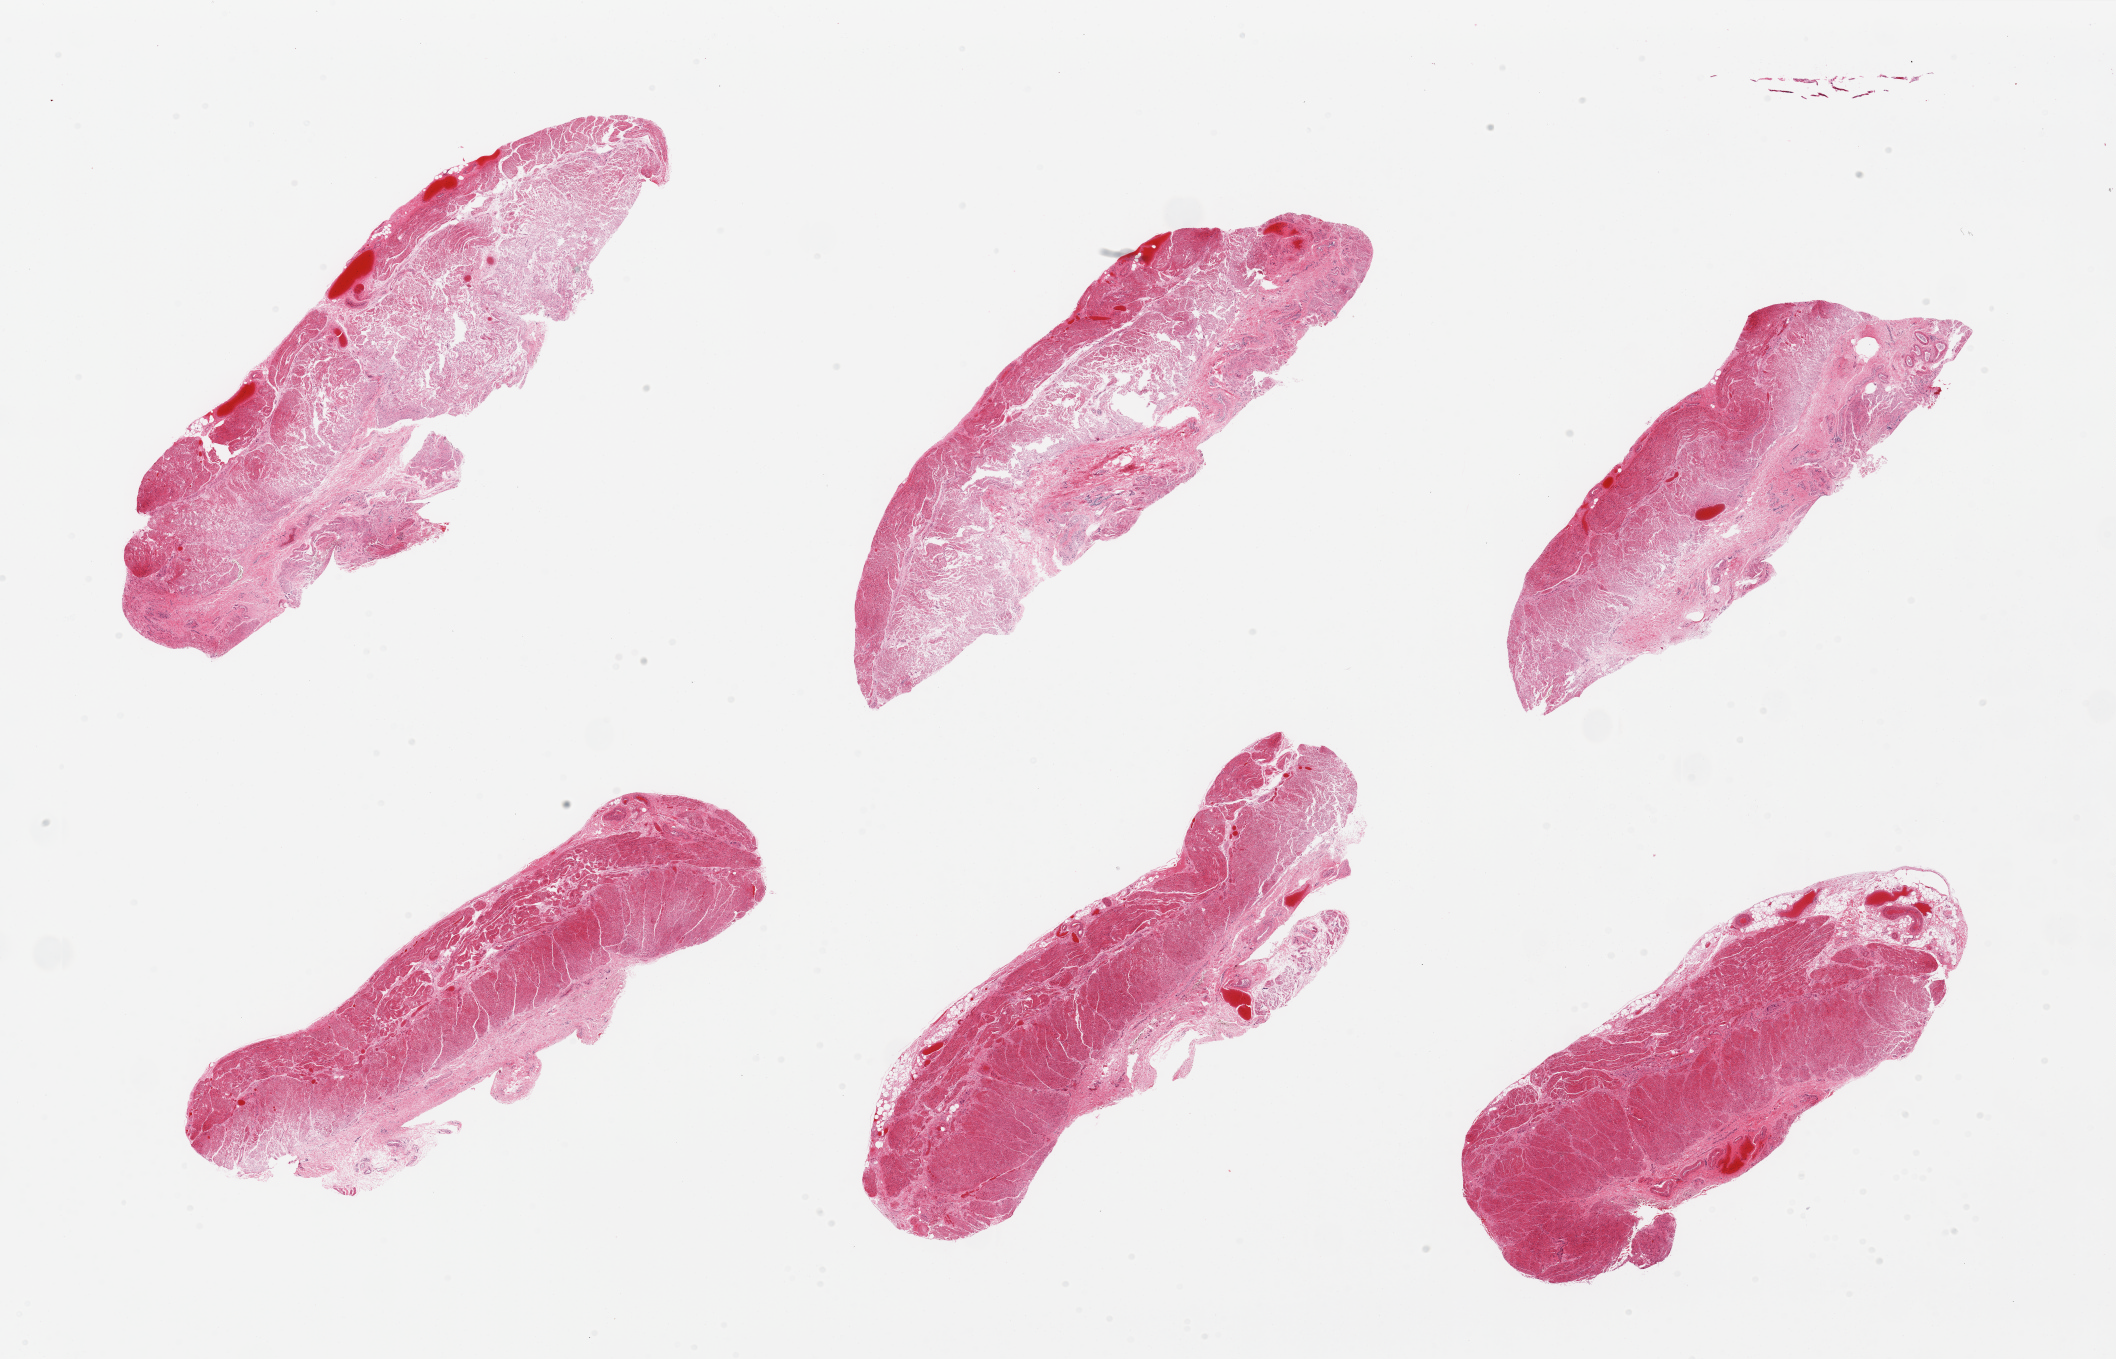
Digitized hematoxylin and eosin (H&E)-stained section, brightfield, low-resolution overview of the scanned area, about 33.5 x 21.5 mm; PAXgene-fixed paraffin-embedded (PFPE) section; section of gastroesophageal junction (target tissue); tissue donor sample. Donor: male.
Pathologist's review note for this sample: 6 pieces, moderately autolyzed/congested; all muscularis.